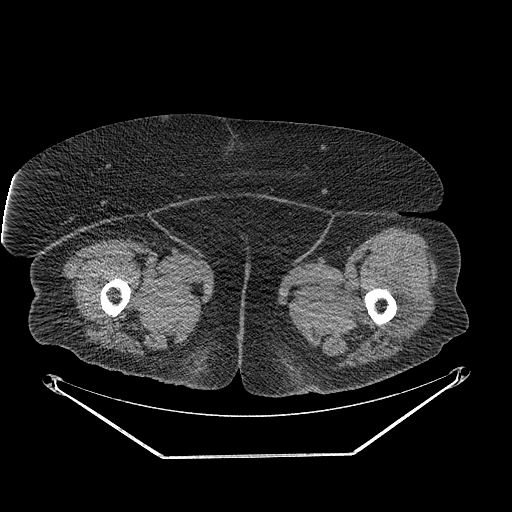
CT of an extremity soft-tissue mass (from a PET/CT study), one axial slice; position 258 of 267 along the scan axis; reconstruction kernel STANDARD; soft-tissue window (W 400 / L 40 HU); 3.75 mm slice thickness; 512 × 512 image matrix, field of view 500 × 500 mm. Female patient. From the clinical record (not read from this slice): histological type: undifferentiated – high grade; grade: high; site of the primary tumour: left thigh.
Annotated regions visible in this slice (expert contour drawn on MRI and transferred to this co-registered scan by the dataset authors):
- gross tumour volume including surrounding oedema: bounding box <390,288,417,330> (left, top, right, bottom; pixels)